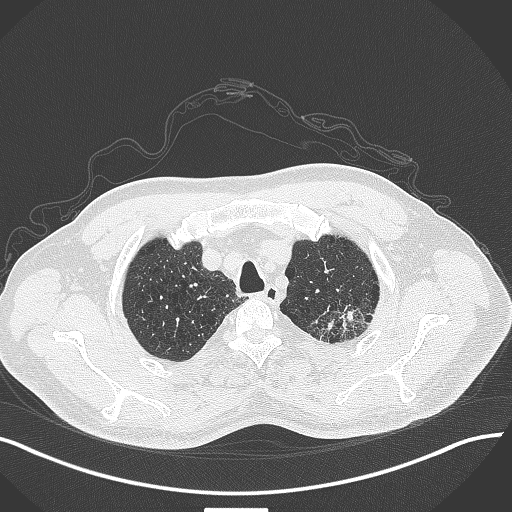
Chest CT, one axial slice. Position 362 of 429 along the scan axis. 120 kVp. Lung window (W 1500 / L -600 HU). 512 × 512 image matrix. Male patient, age 55 years. From the clinical record (not read from this slice): clinical TNM (as recorded): T3 N0 M1c; histopathological grade: G3.
Annotated regions visible in this slice (bounding box drawn by a radiologist):
- lung tumour (recorded histology: adenocarcinoma): bounding box [x1, y1, x2, y2] px = [309, 301, 383, 350]